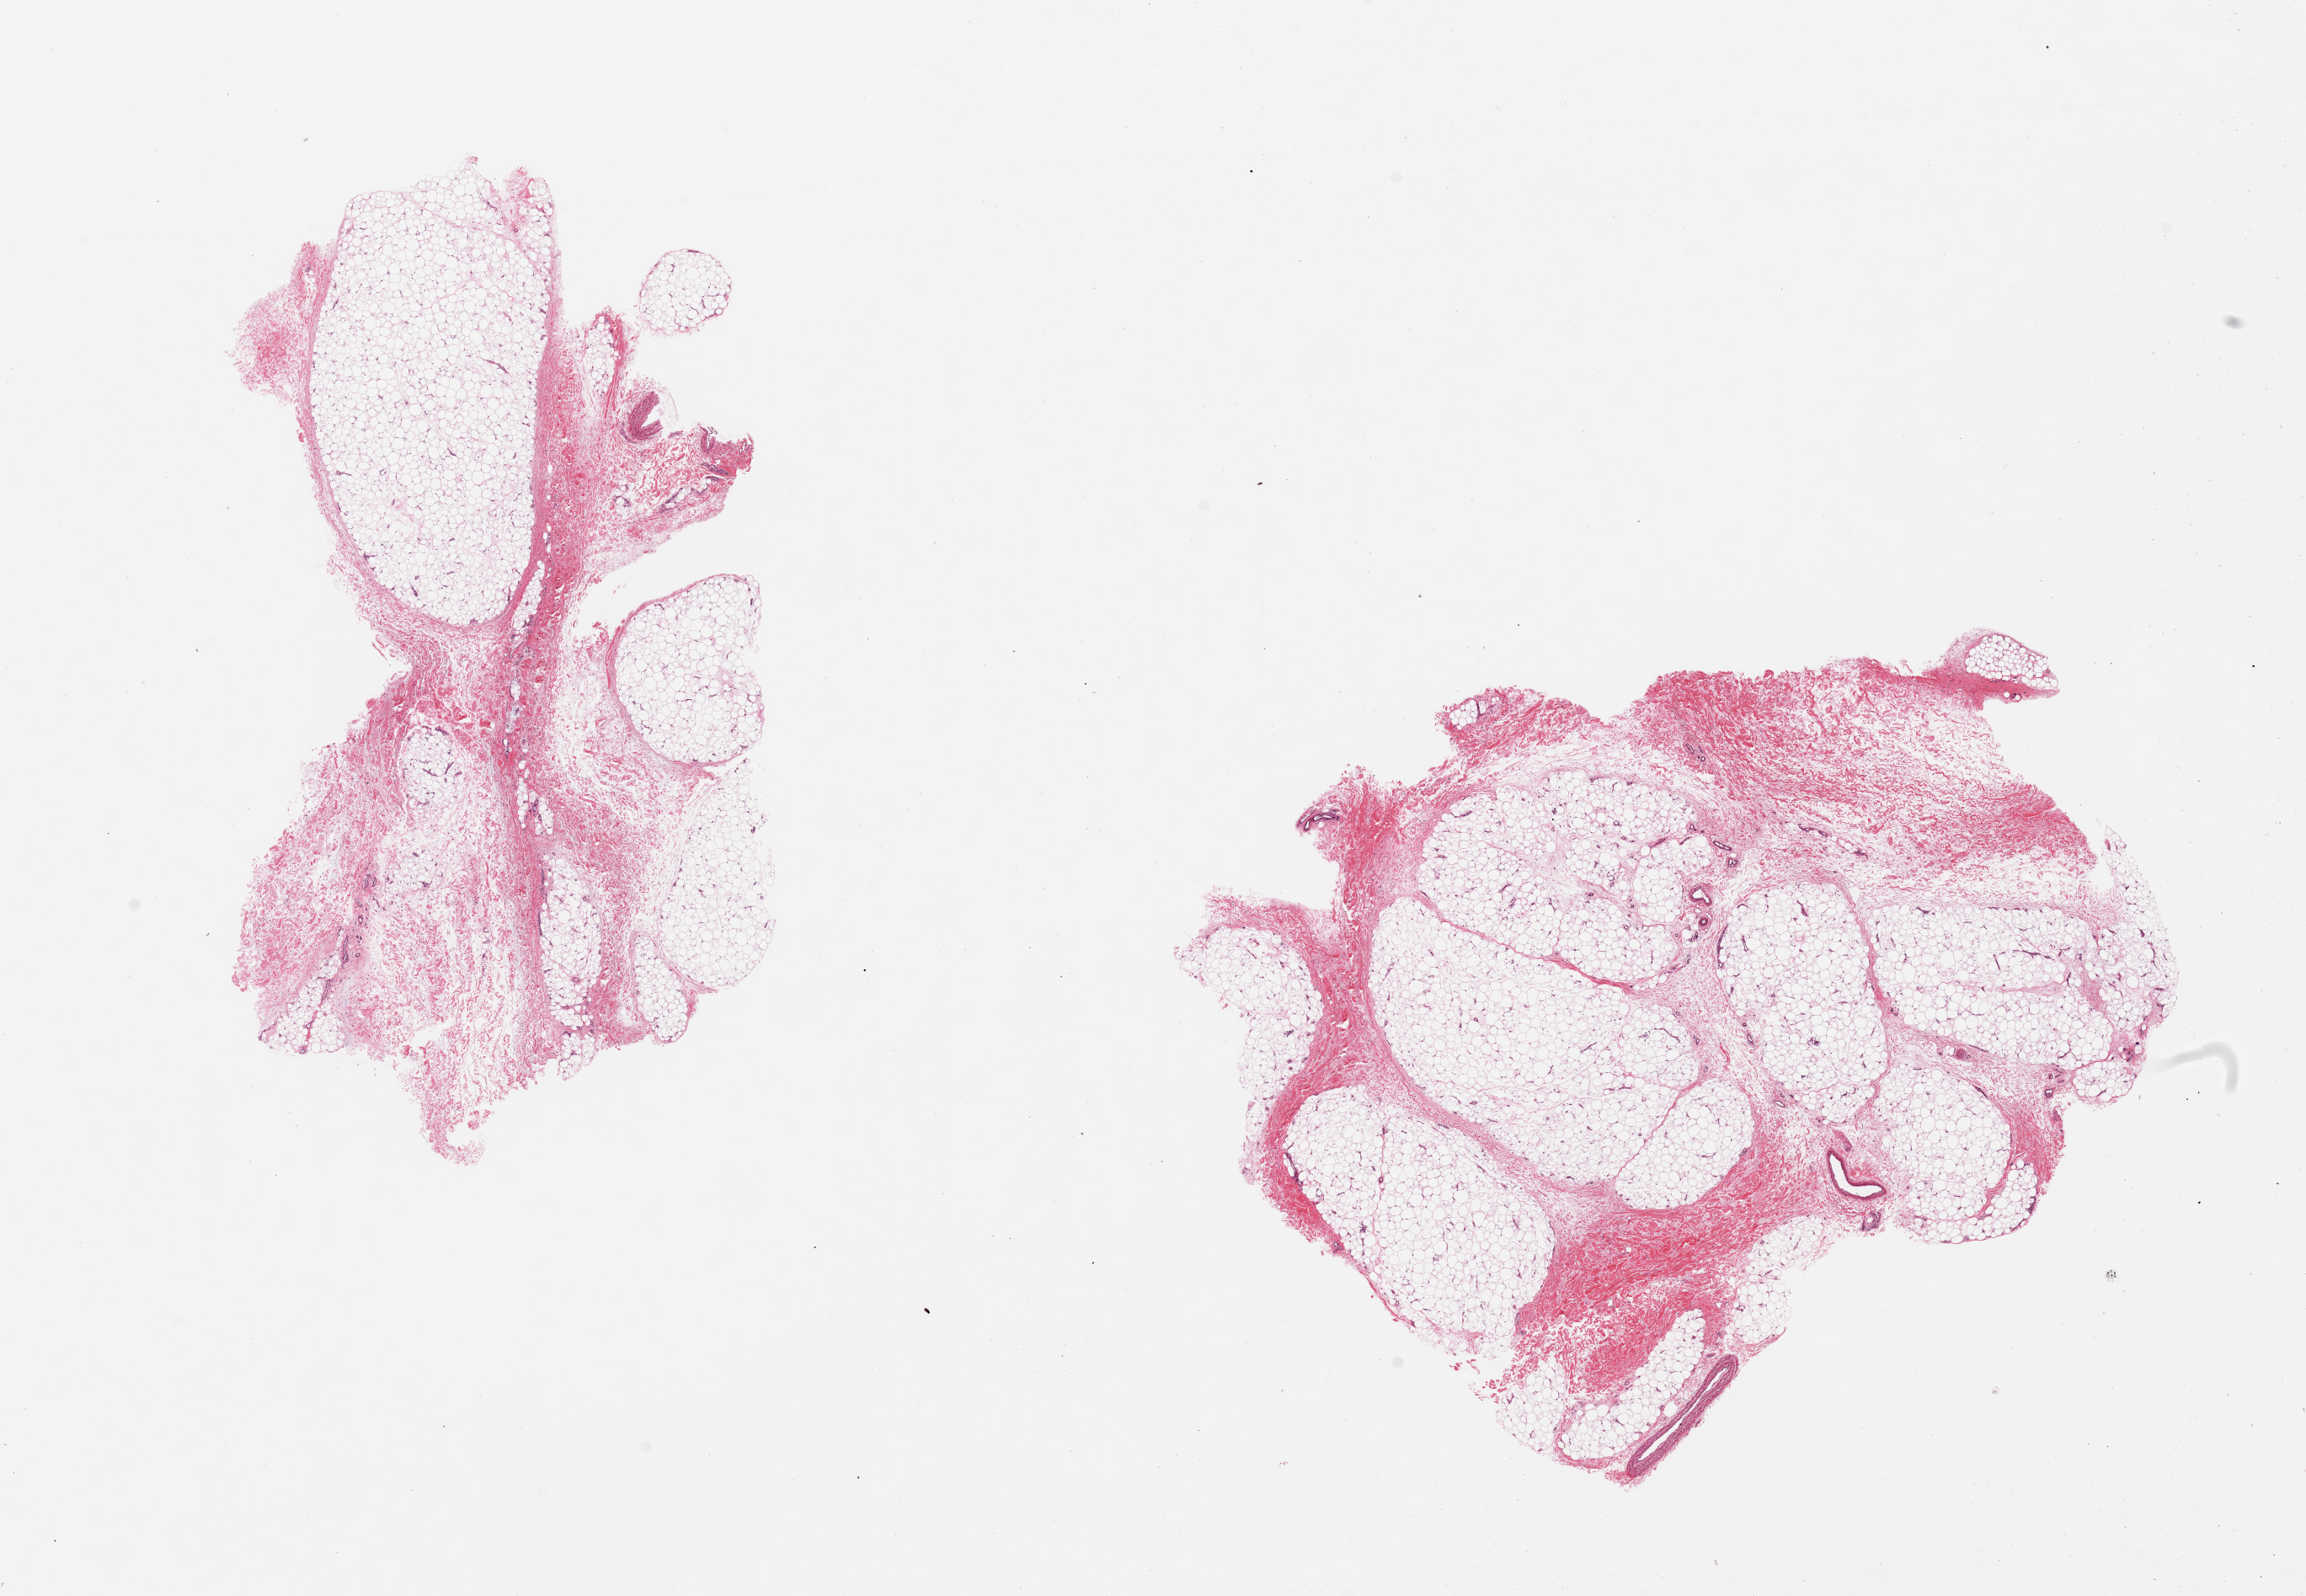
Whole-slide image, hematoxylin and eosin (H&E) stain, a low-resolution overview of the entire scanned area, about 21.7 x 15.0 mm, PAXgene-fixed paraffin-embedded (PFPE) section, section of adipose tissue (target tissue), donor tissue sample.
Pathologist's review note for this sample: 2 pieces, septal fibrosis 20%.